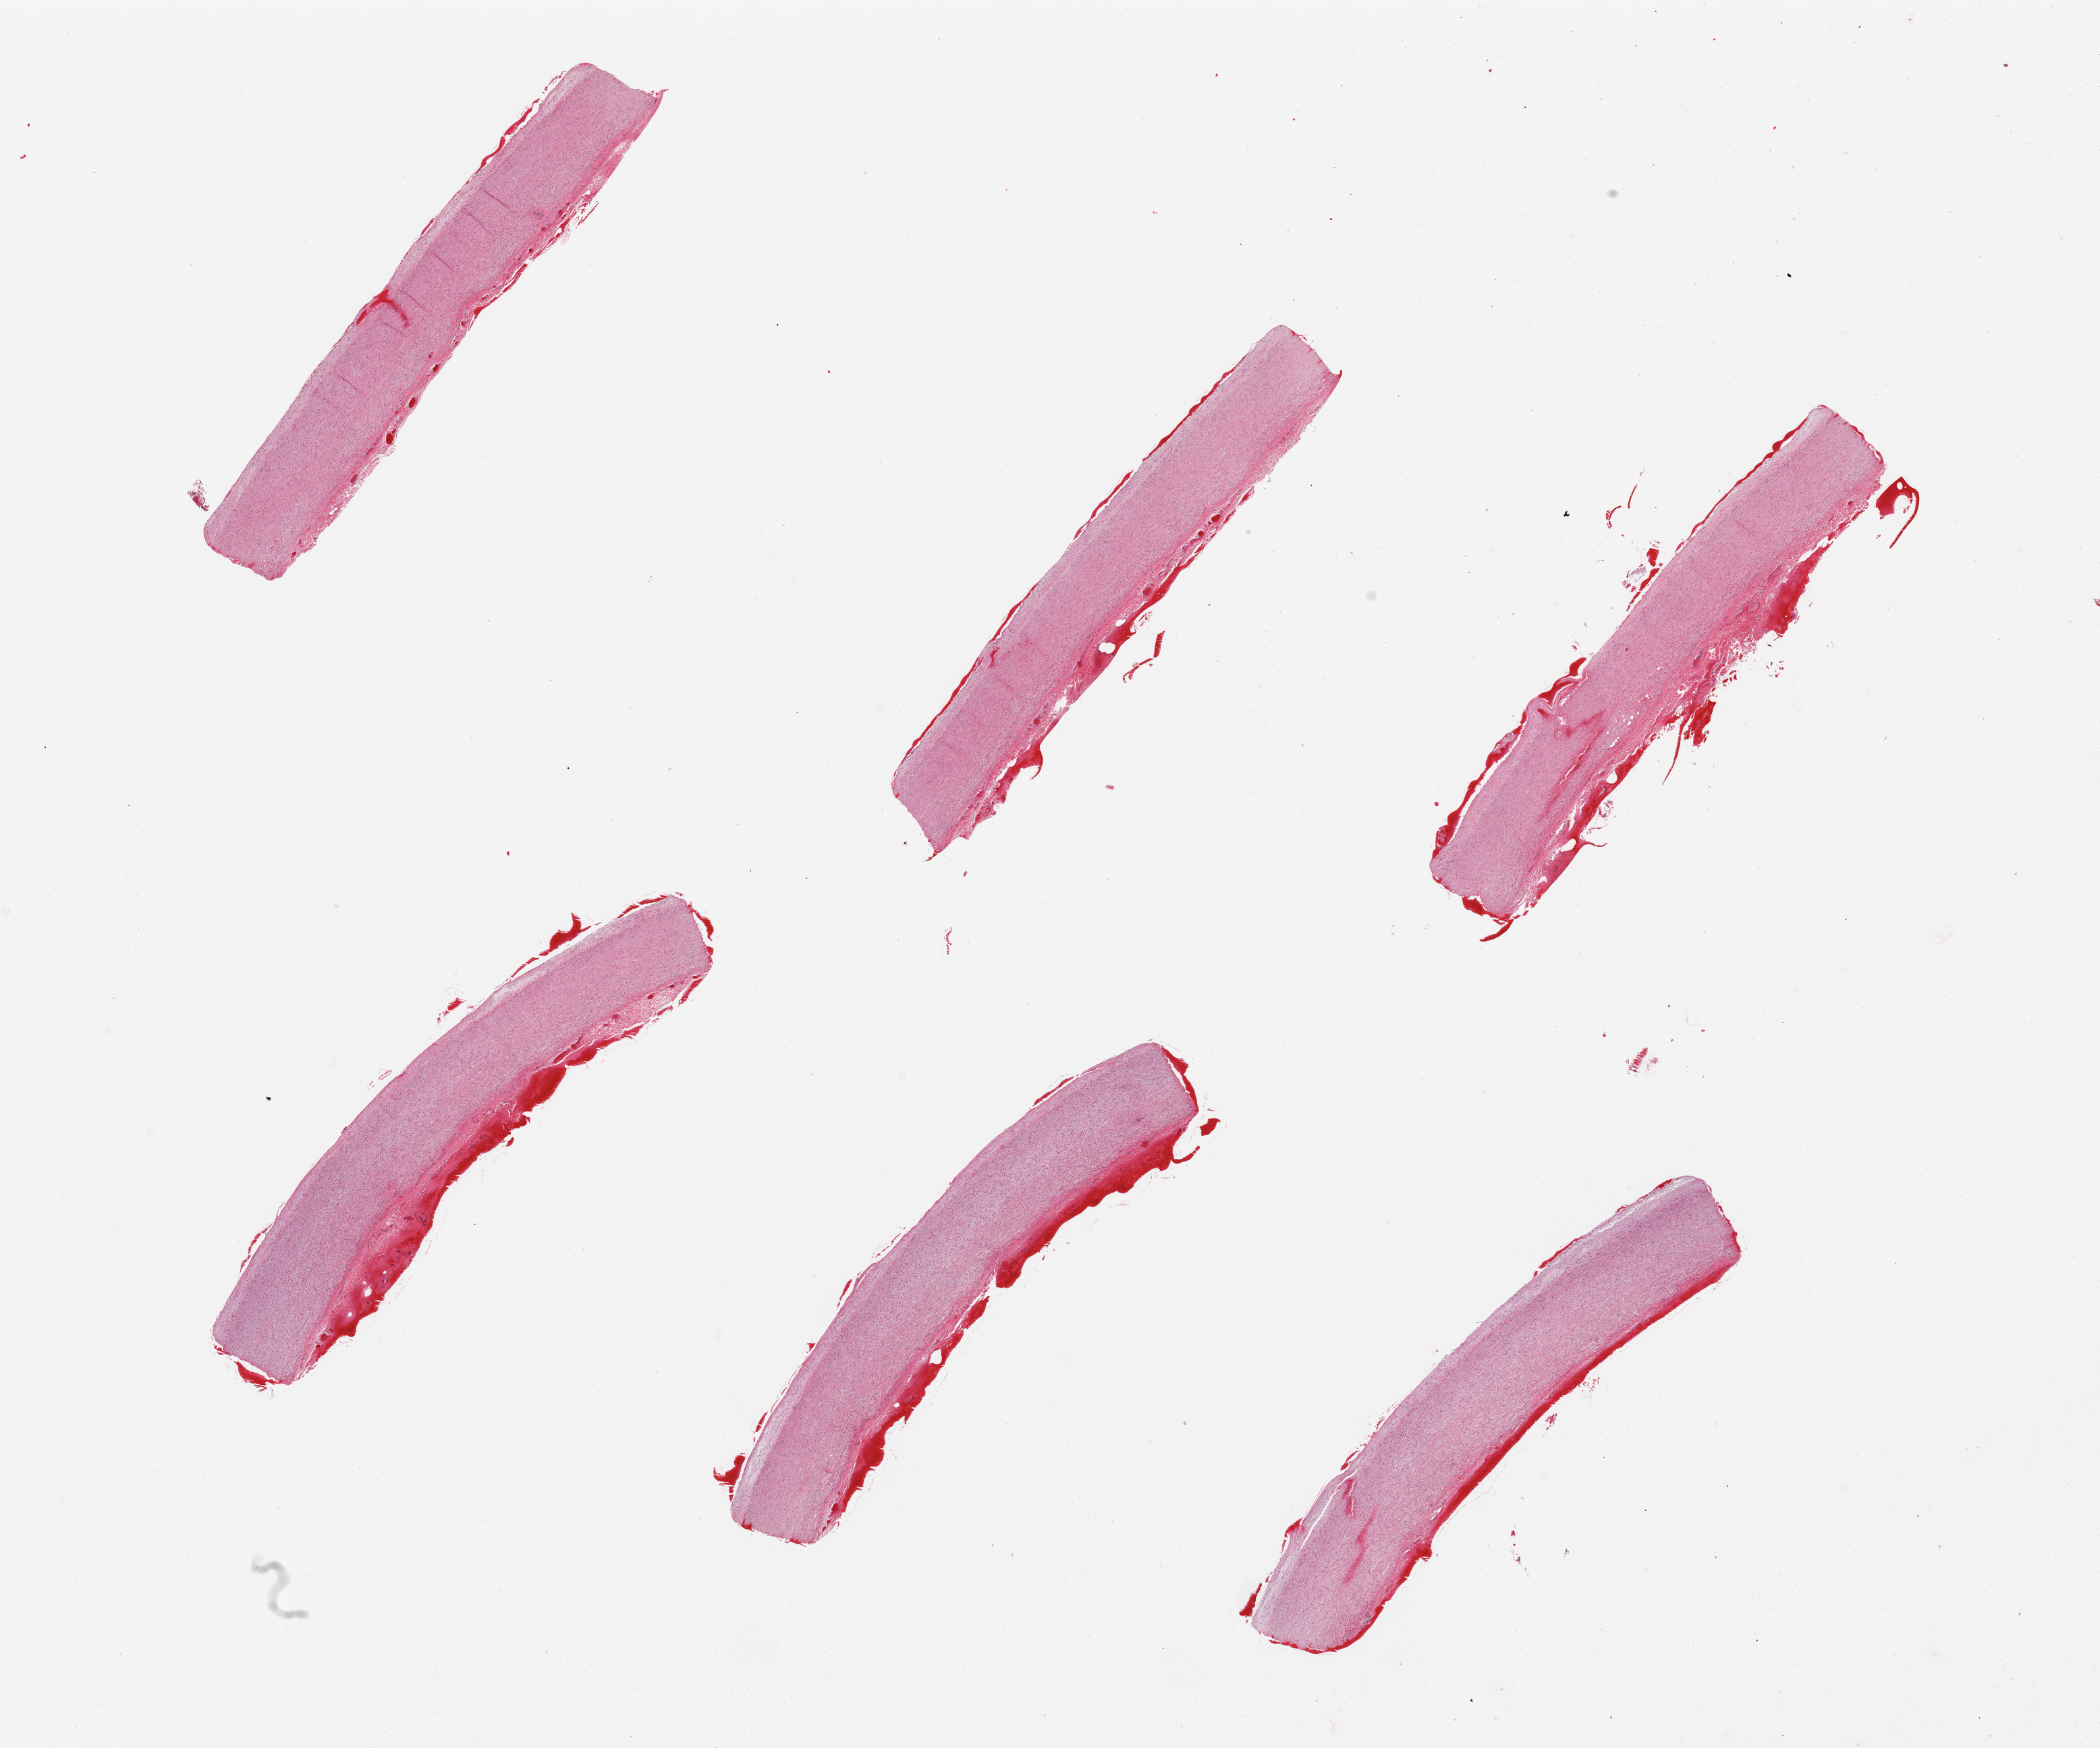
H&E whole-slide image — shown as a low-resolution overview of the whole scanned area (about 24.6 x 20.5 mm, slide scanned at 20x); PAXgene-fixed, paraffin-embedded tissue; sampled site (target tissue): aorta; tissue donor sample. Donor sex: female.
Reviewer comment on this tissue sample: 6 pieces, adherent serosa, ~0.5mm.